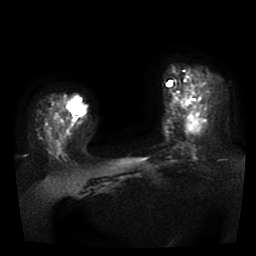
Breast MRI, one axial slice; slice 12 of 41 in the series (ordered by position); diffusion-weighted series; image 2 of 4 stored at this slice position (different b-values; order by instance number); 1.5 T; 256 × 256 image matrix. Female patient.
Structures marked on this image (outlined manually by an expert reader):
- tumour on diffusion-weighted imaging: bounding box <69,97,87,116> (left, top, right, bottom; pixels)